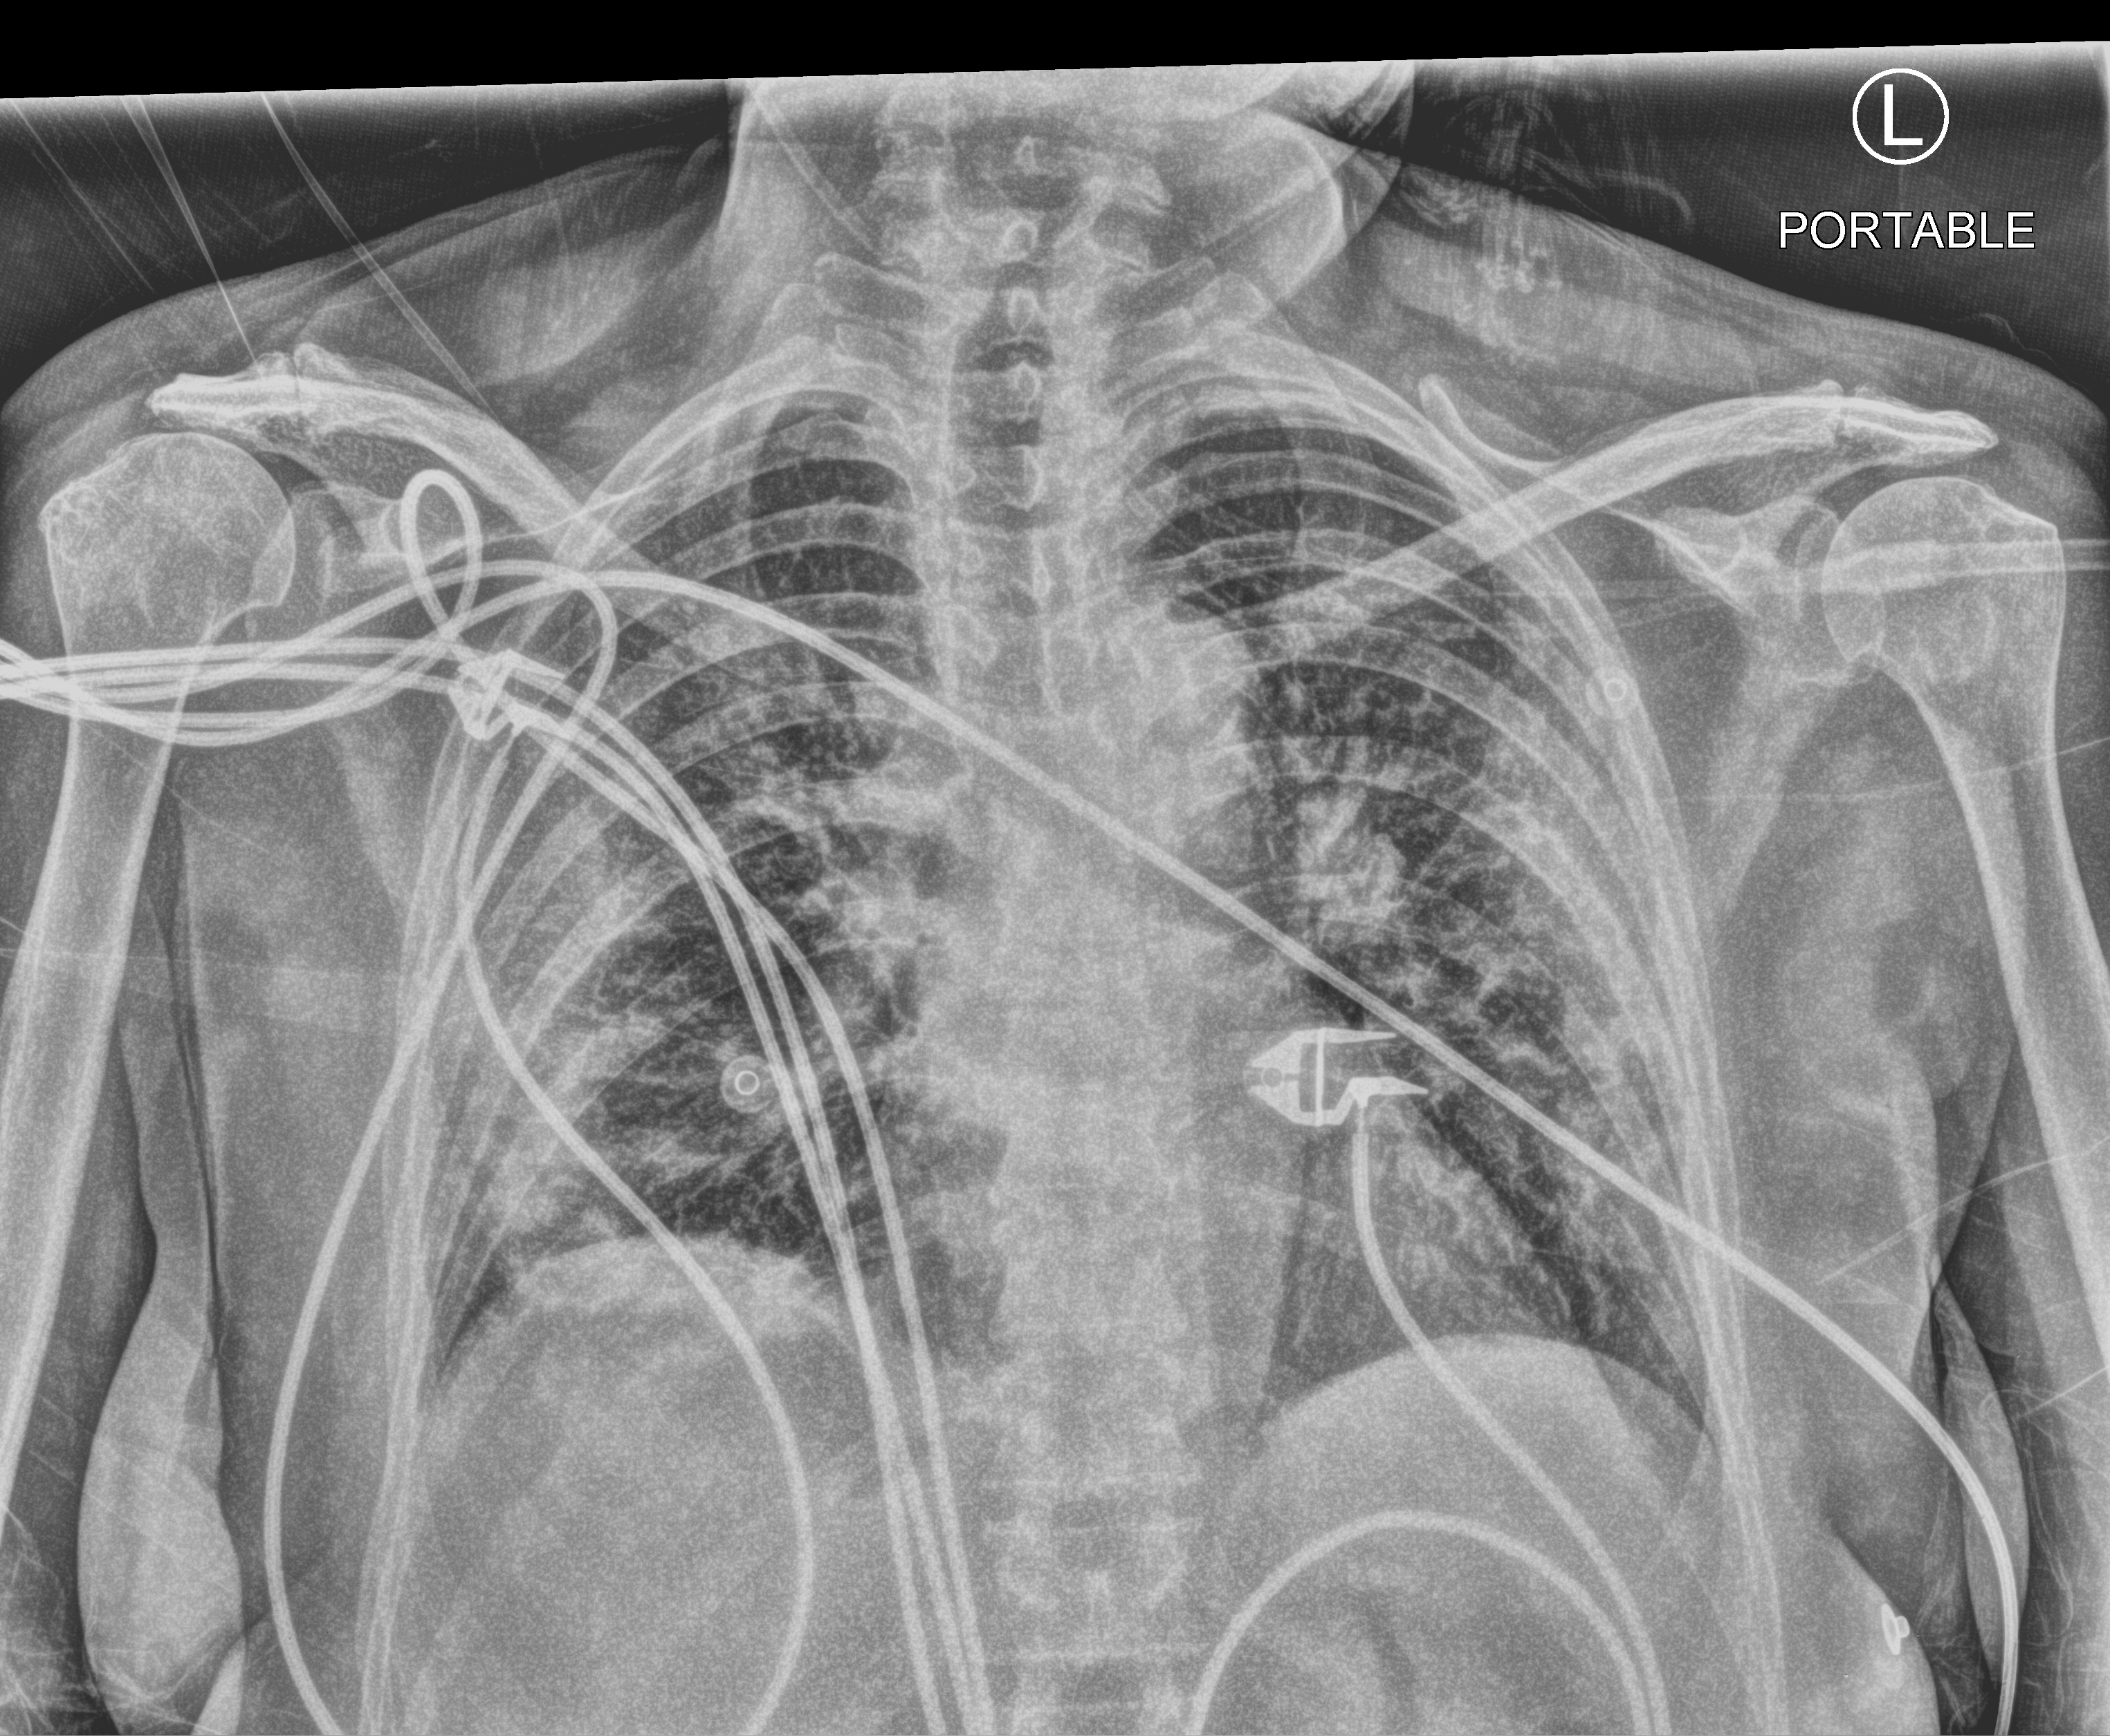
Chest X-ray (portable), anteroposterior (AP) projection. Female patient hospitalised with COVID-19, age 60–74 years.
From the hospital-stay record, not from the radiograph (when in the stay this image was taken is not recorded): mechanically ventilated during this hospital stay: yes; chronic kidney disease (admission record): no.